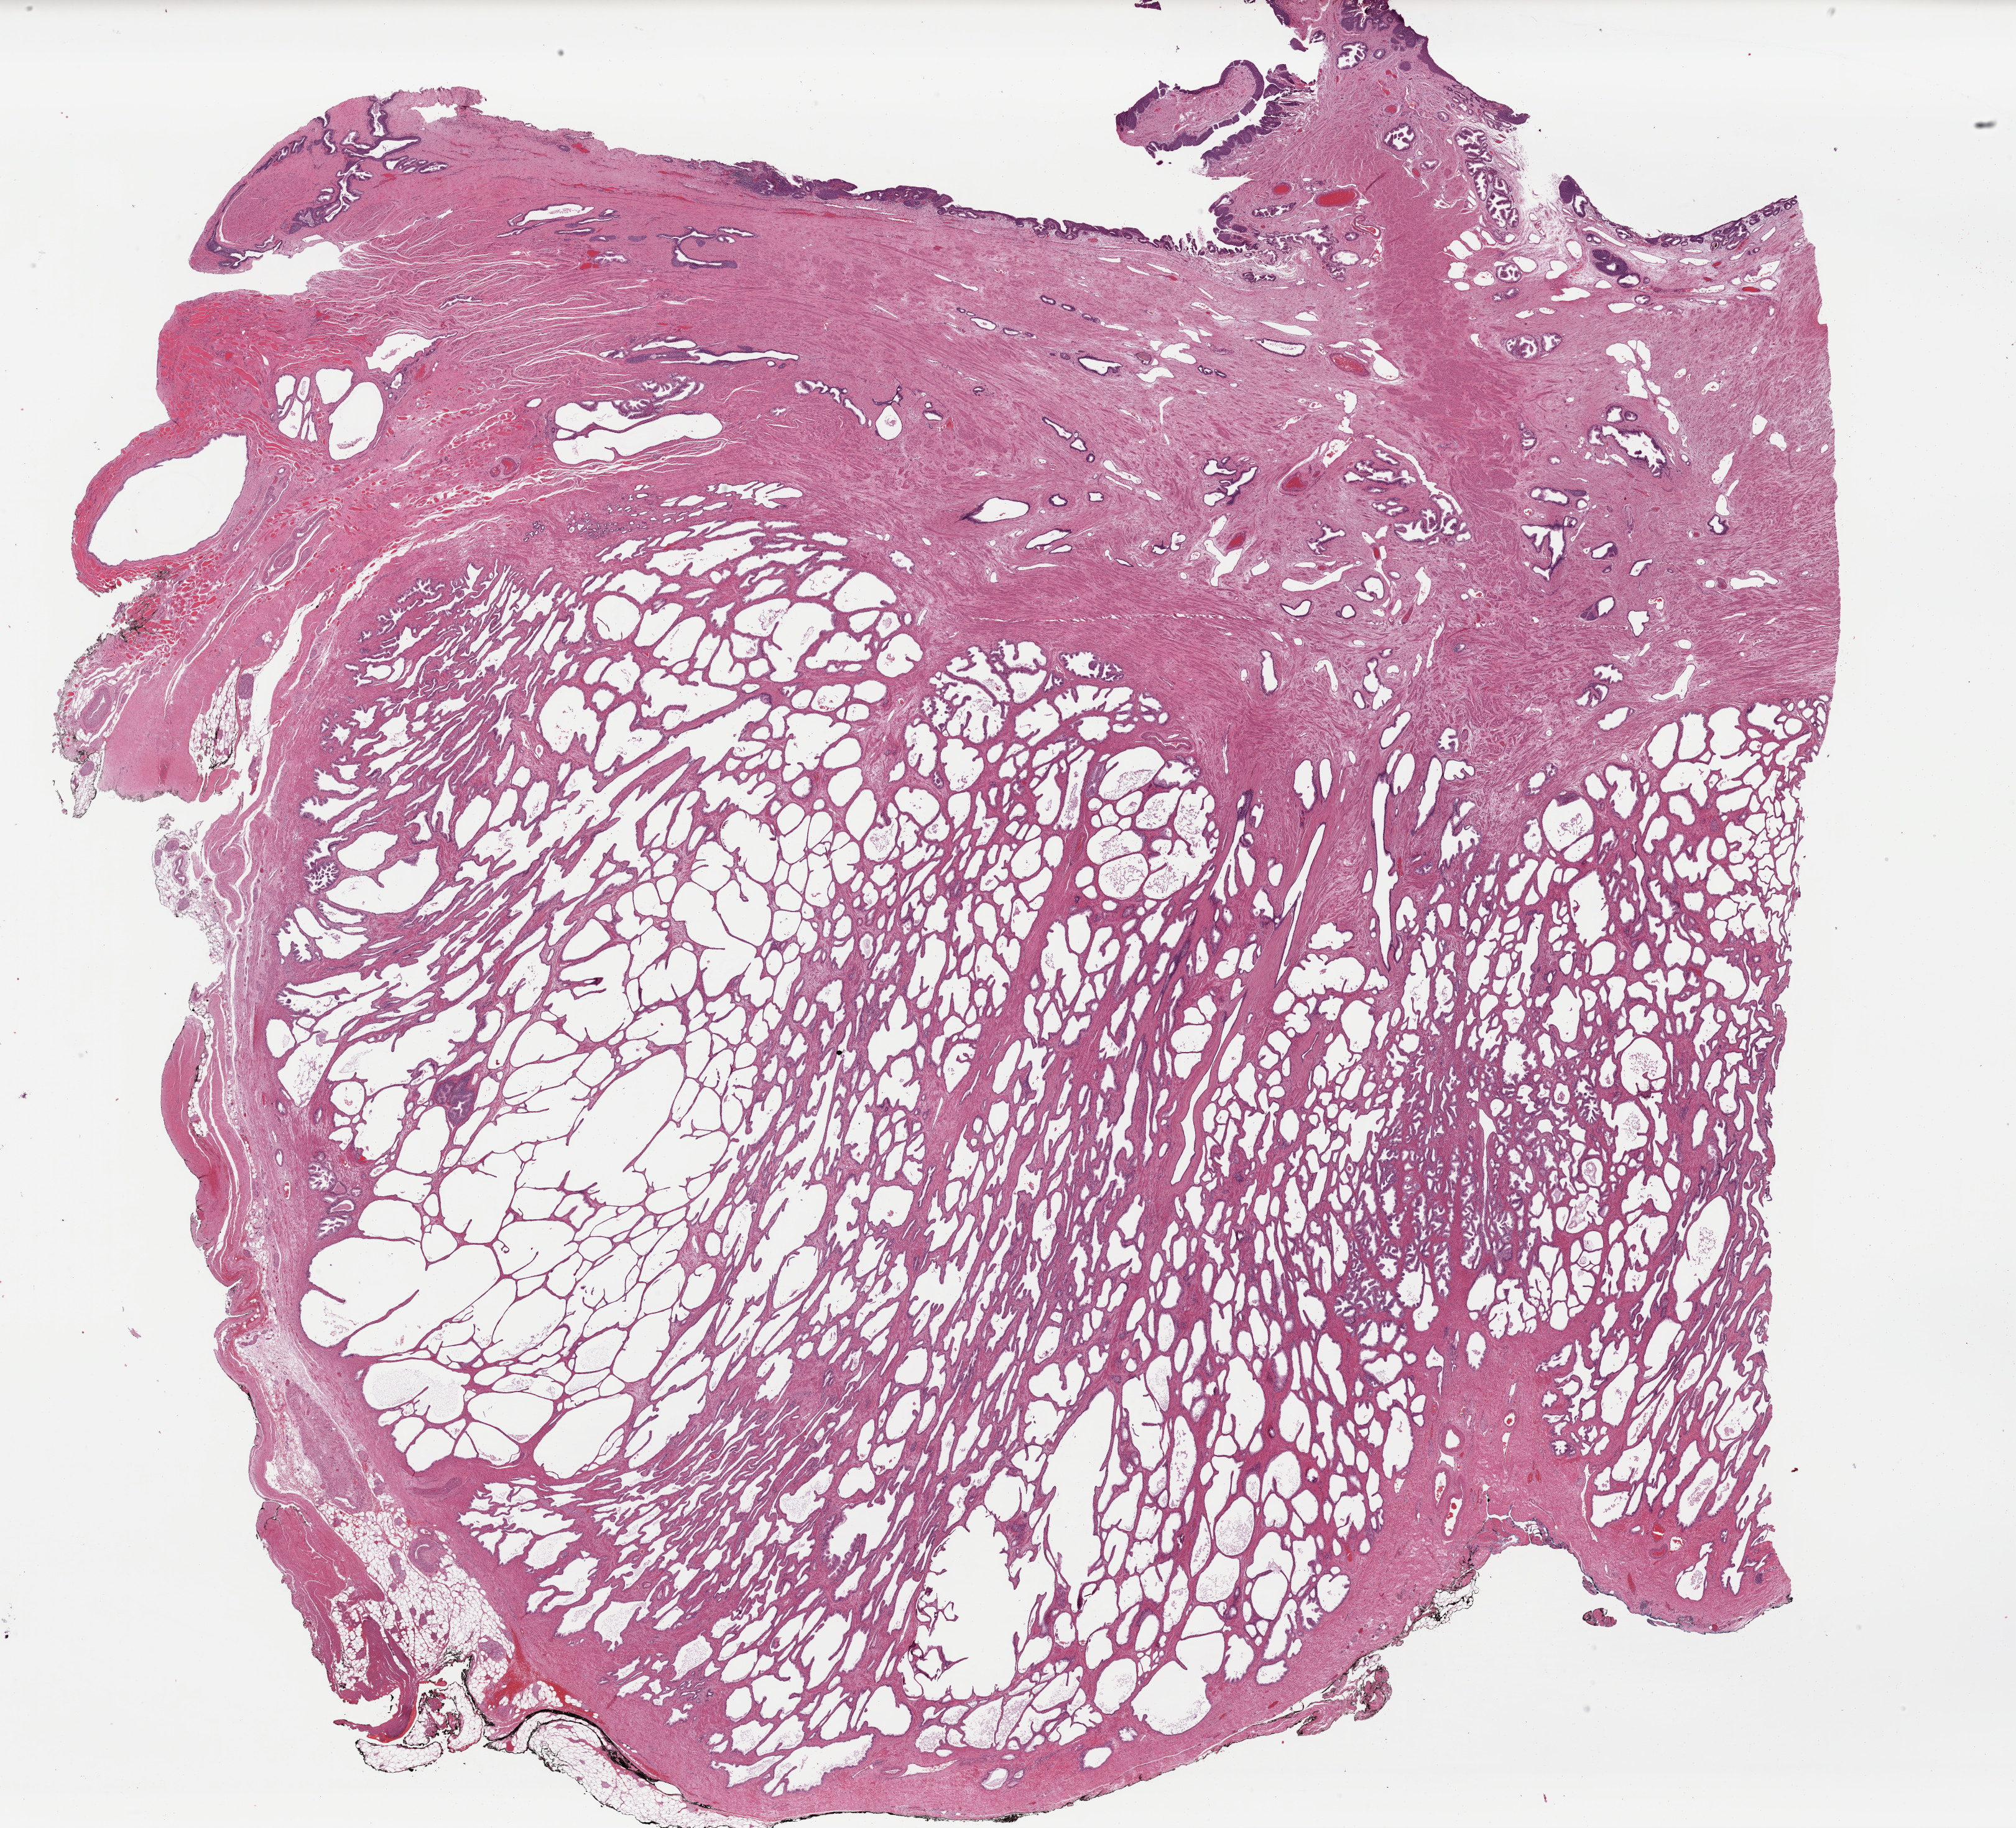
H&E whole-slide image — whole scanned area (about 25.6 x 23.2 mm) shown as a low-resolution overview; formalin-fixed paraffin-embedded (FFPE) diagnostic section; sample: primary tumour, bladder. Patient: male, age at initial diagnosis 75 years. Histologic grade: high grade.
Lymph nodes positive (case pathology): 0 of 15 examined. Histologic diagnosis: Papillary transitional cell carcinoma (posterior wall of bladder). TNM: T2b N0 MX. AJCC pathologic stage: II (7th edition).